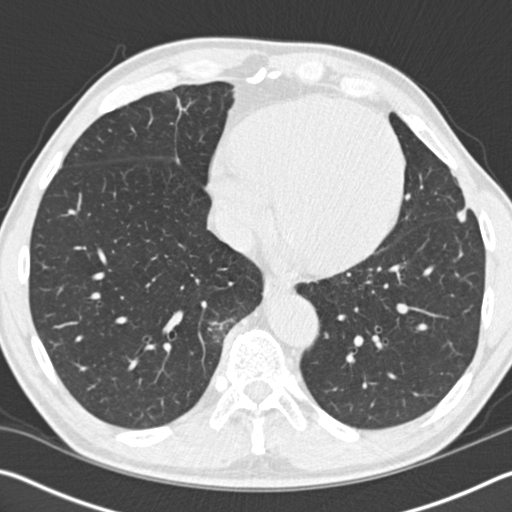
Low-dose screening chest CT, one axial slice. Slice 48 of 162 in the series (ordered by position). Reconstruction kernel B30f. 120 kVp. Lung window (W 1500 / L -600 HU). 2 mm slice thickness. 512 × 512 image matrix, field of view 340 × 340 mm.
Structures marked on this image (manually delineated by an expert):
- lesion 1 (tumor, upper lobe of left lung): bounding box <457,207,468,222> (left, top, right, bottom; pixels)